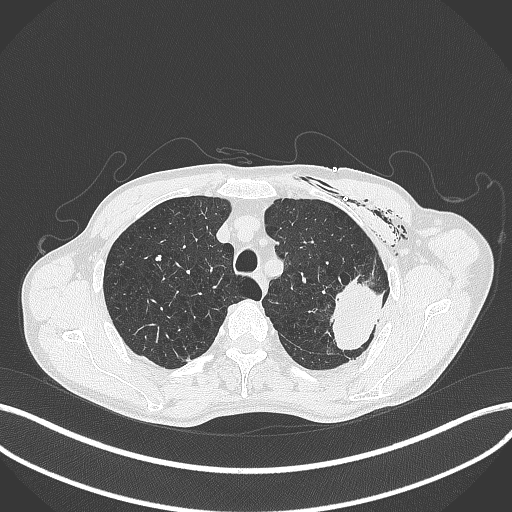
Chest CT, one axial slice; position 327 of 457 along the scan axis; reconstruction kernel B70f; 120 kVp; lung window (W 1500 / L -600 HU); 1 mm slice thickness; 512 × 512 image matrix, field of view 400 × 400 mm. Patient: male, 58 years. From the clinical record (not read from this slice): clinical TNM (as recorded): T3 N0 M0.
Outlined on this slice (rectangle marked by the reading radiologist):
- lung tumour (recorded histology: adenocarcinoma): bounding box (x1, y1, x2, y2) in pixels: (326, 275, 387, 354)